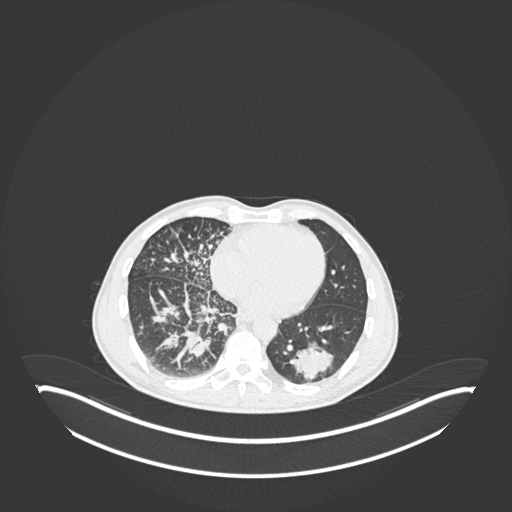
Chest CT, one axial slice. Lung window (W 1500 / L -600 HU). 1 mm slice thickness. 512 × 512 image matrix, field of view 500 × 500 mm. Male patient, age 49 years. Case-level facts recorded for this patient, not image findings: clinical TNM (as recorded): T2b N1 M0.
Outlined on this slice (rectangle marked by the reading radiologist):
- lung tumour (recorded histology: adenocarcinoma): bounding box <287,339,336,380> (left, top, right, bottom; pixels)